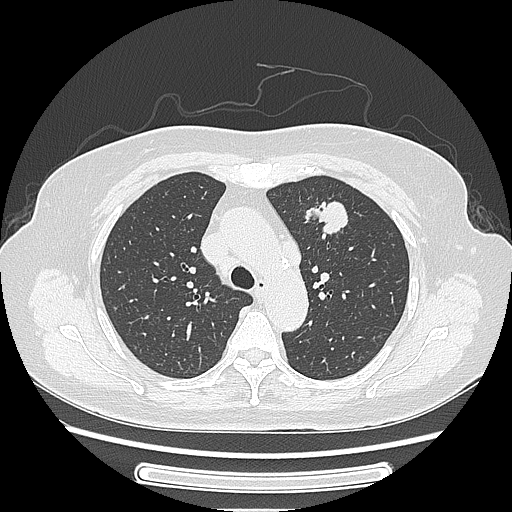
Chest CT, one axial slice; reconstruction kernel LUNG; 120 kVp; lung window (W 1500 / L -600 HU); 1.25 mm slice thickness; 512 × 512 image matrix, field of view 363 × 363 mm. Female patient, age 77 years. From the clinical record (not read from this slice): clinical TNM (as recorded): T1c N3 M0; histopathological grade: G2-3.
Structures marked on this image (bounding box drawn by a radiologist):
- lung tumour (recorded histology: adenocarcinoma): bounding box <308,186,357,240> (left, top, right, bottom; pixels)